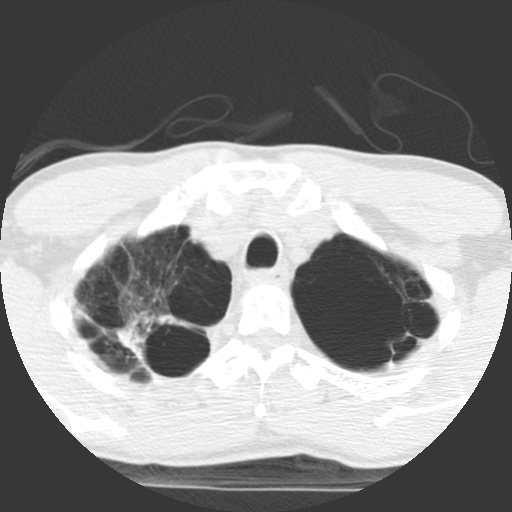
Chest CT (low-dose screening protocol), one axial image, baseline screening round, lung window (W 1500 / L -600 HU), 2.5 mm slice thickness, standard (soft-tissue) reconstruction kernel (STANDARD), slice 96 of 117 in the series. Male participant, aged 62 years at enrolment.
- Expert-annotated lung lesion, bounding box [x1, y1, x2, y2] px = [110, 303, 214, 387].
- No non-calcified nodule or mass ≥4 mm was recorded by the screening reader at this exam.
- Official screen result: negative screen, minor abnormalities not suspicious for lung cancer.
- Participant outcome: lung cancer diagnosed 357 days after this screen — non-small cell carcinoma, right upper lobe, poorly differentiated (G3), stage IA (AJCC 6th edition), 70 mm at pathology.